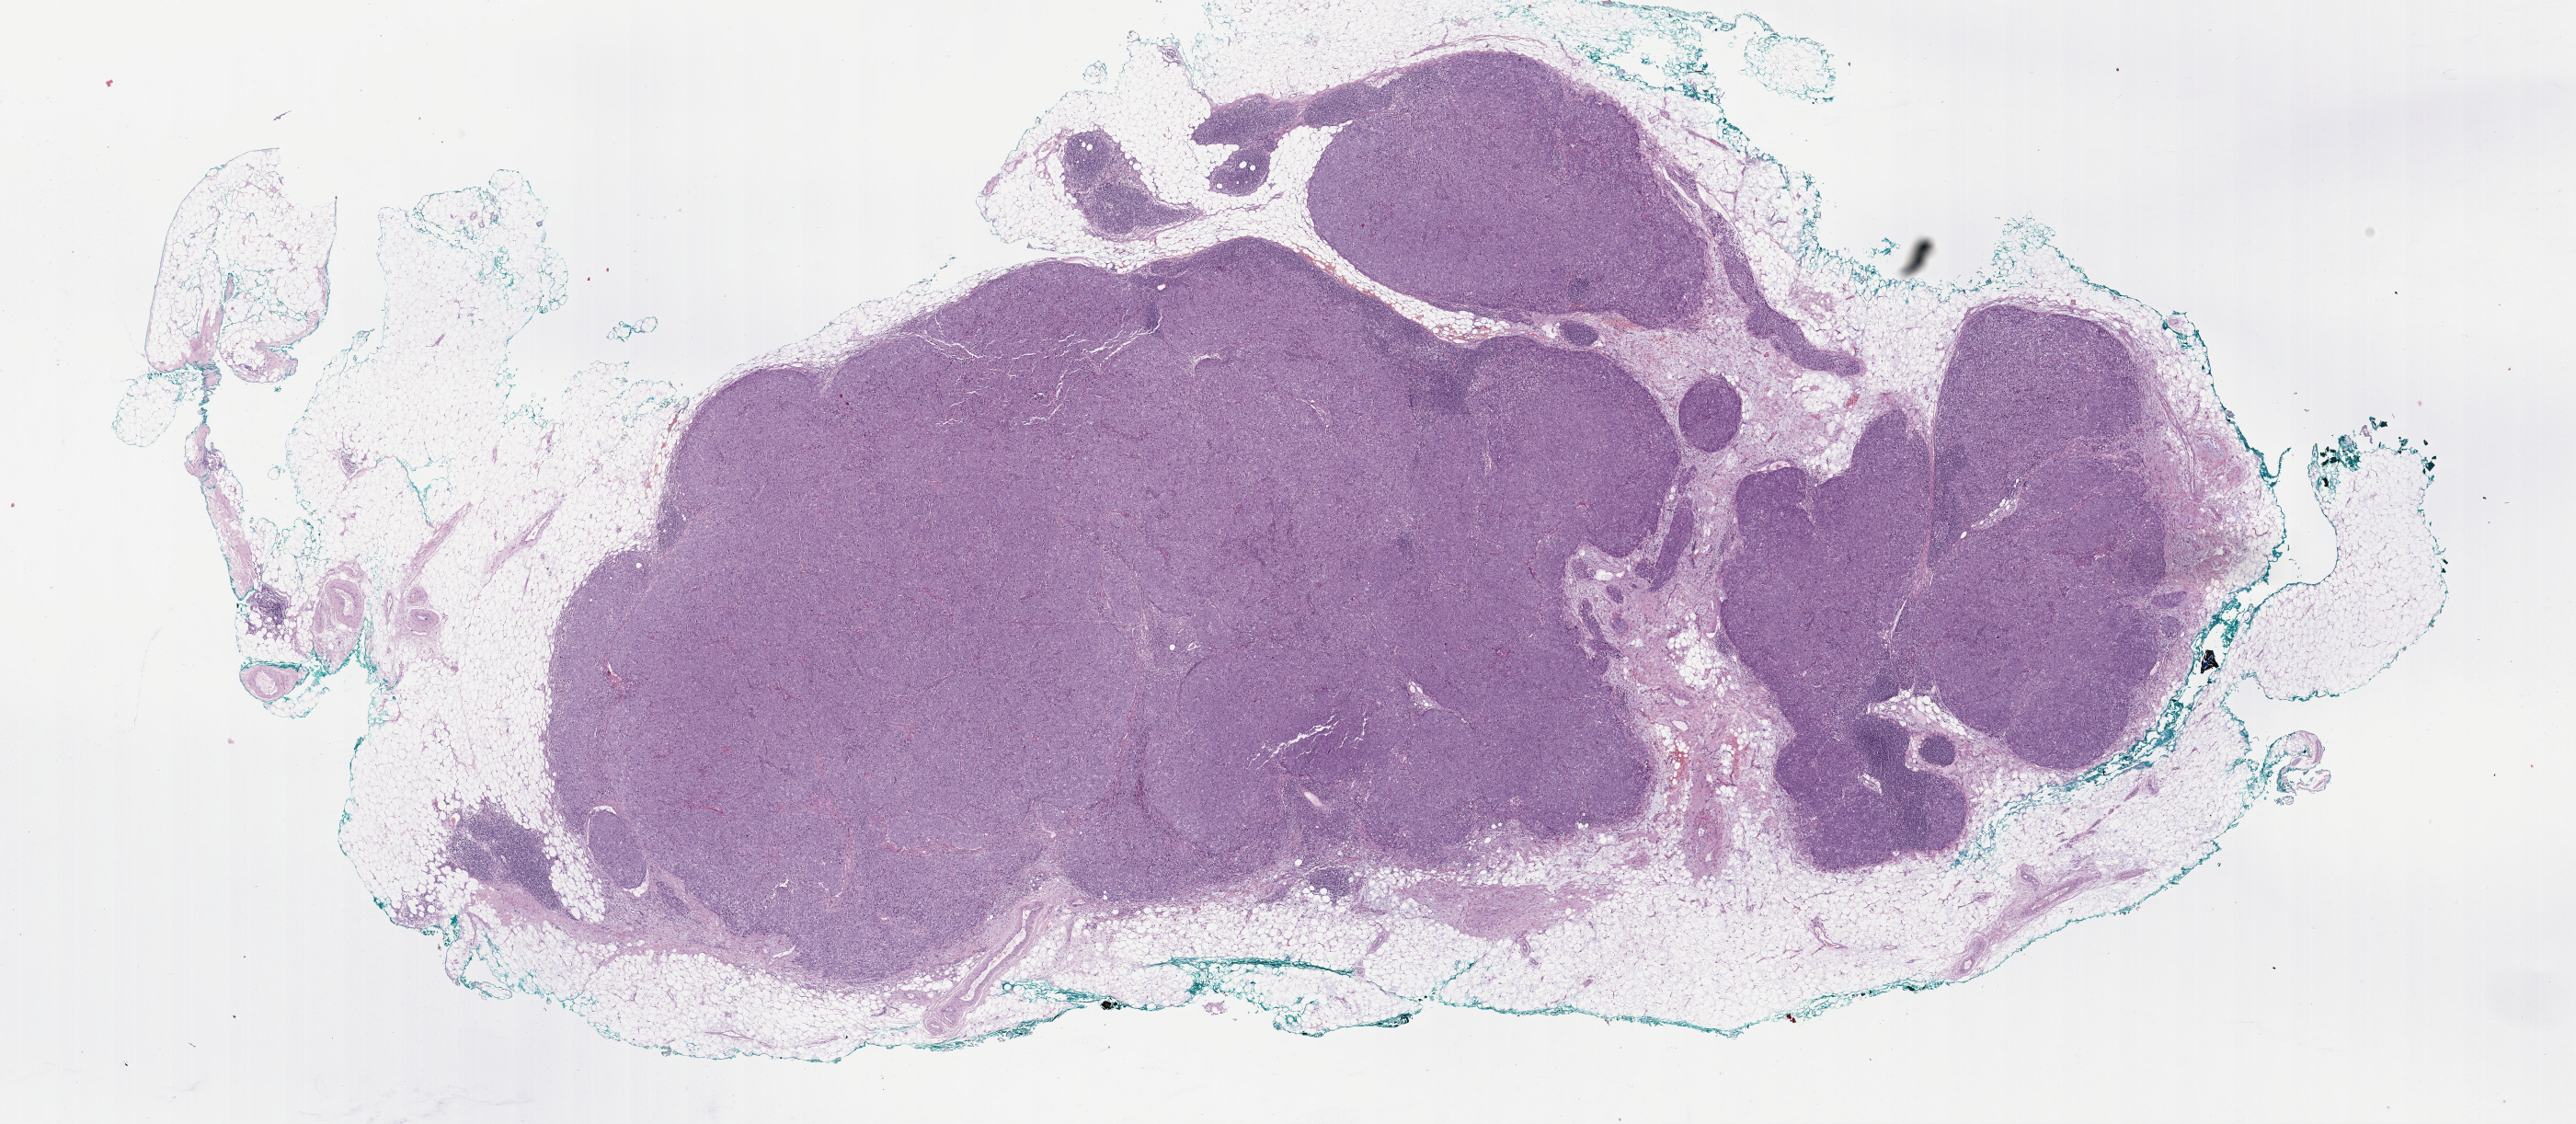
Whole-slide histology image, Hematoxylin and eosin (H&E) stained — whole scanned area (about 22.7 x 9.9 mm) shown as a low-resolution overview, formalin-fixed paraffin-embedded (FFPE) diagnostic section, primary tumour sample from the thymus. Male, age 63 years at initial diagnosis.
Diagnosis: Thymic carcinoma, NOS.